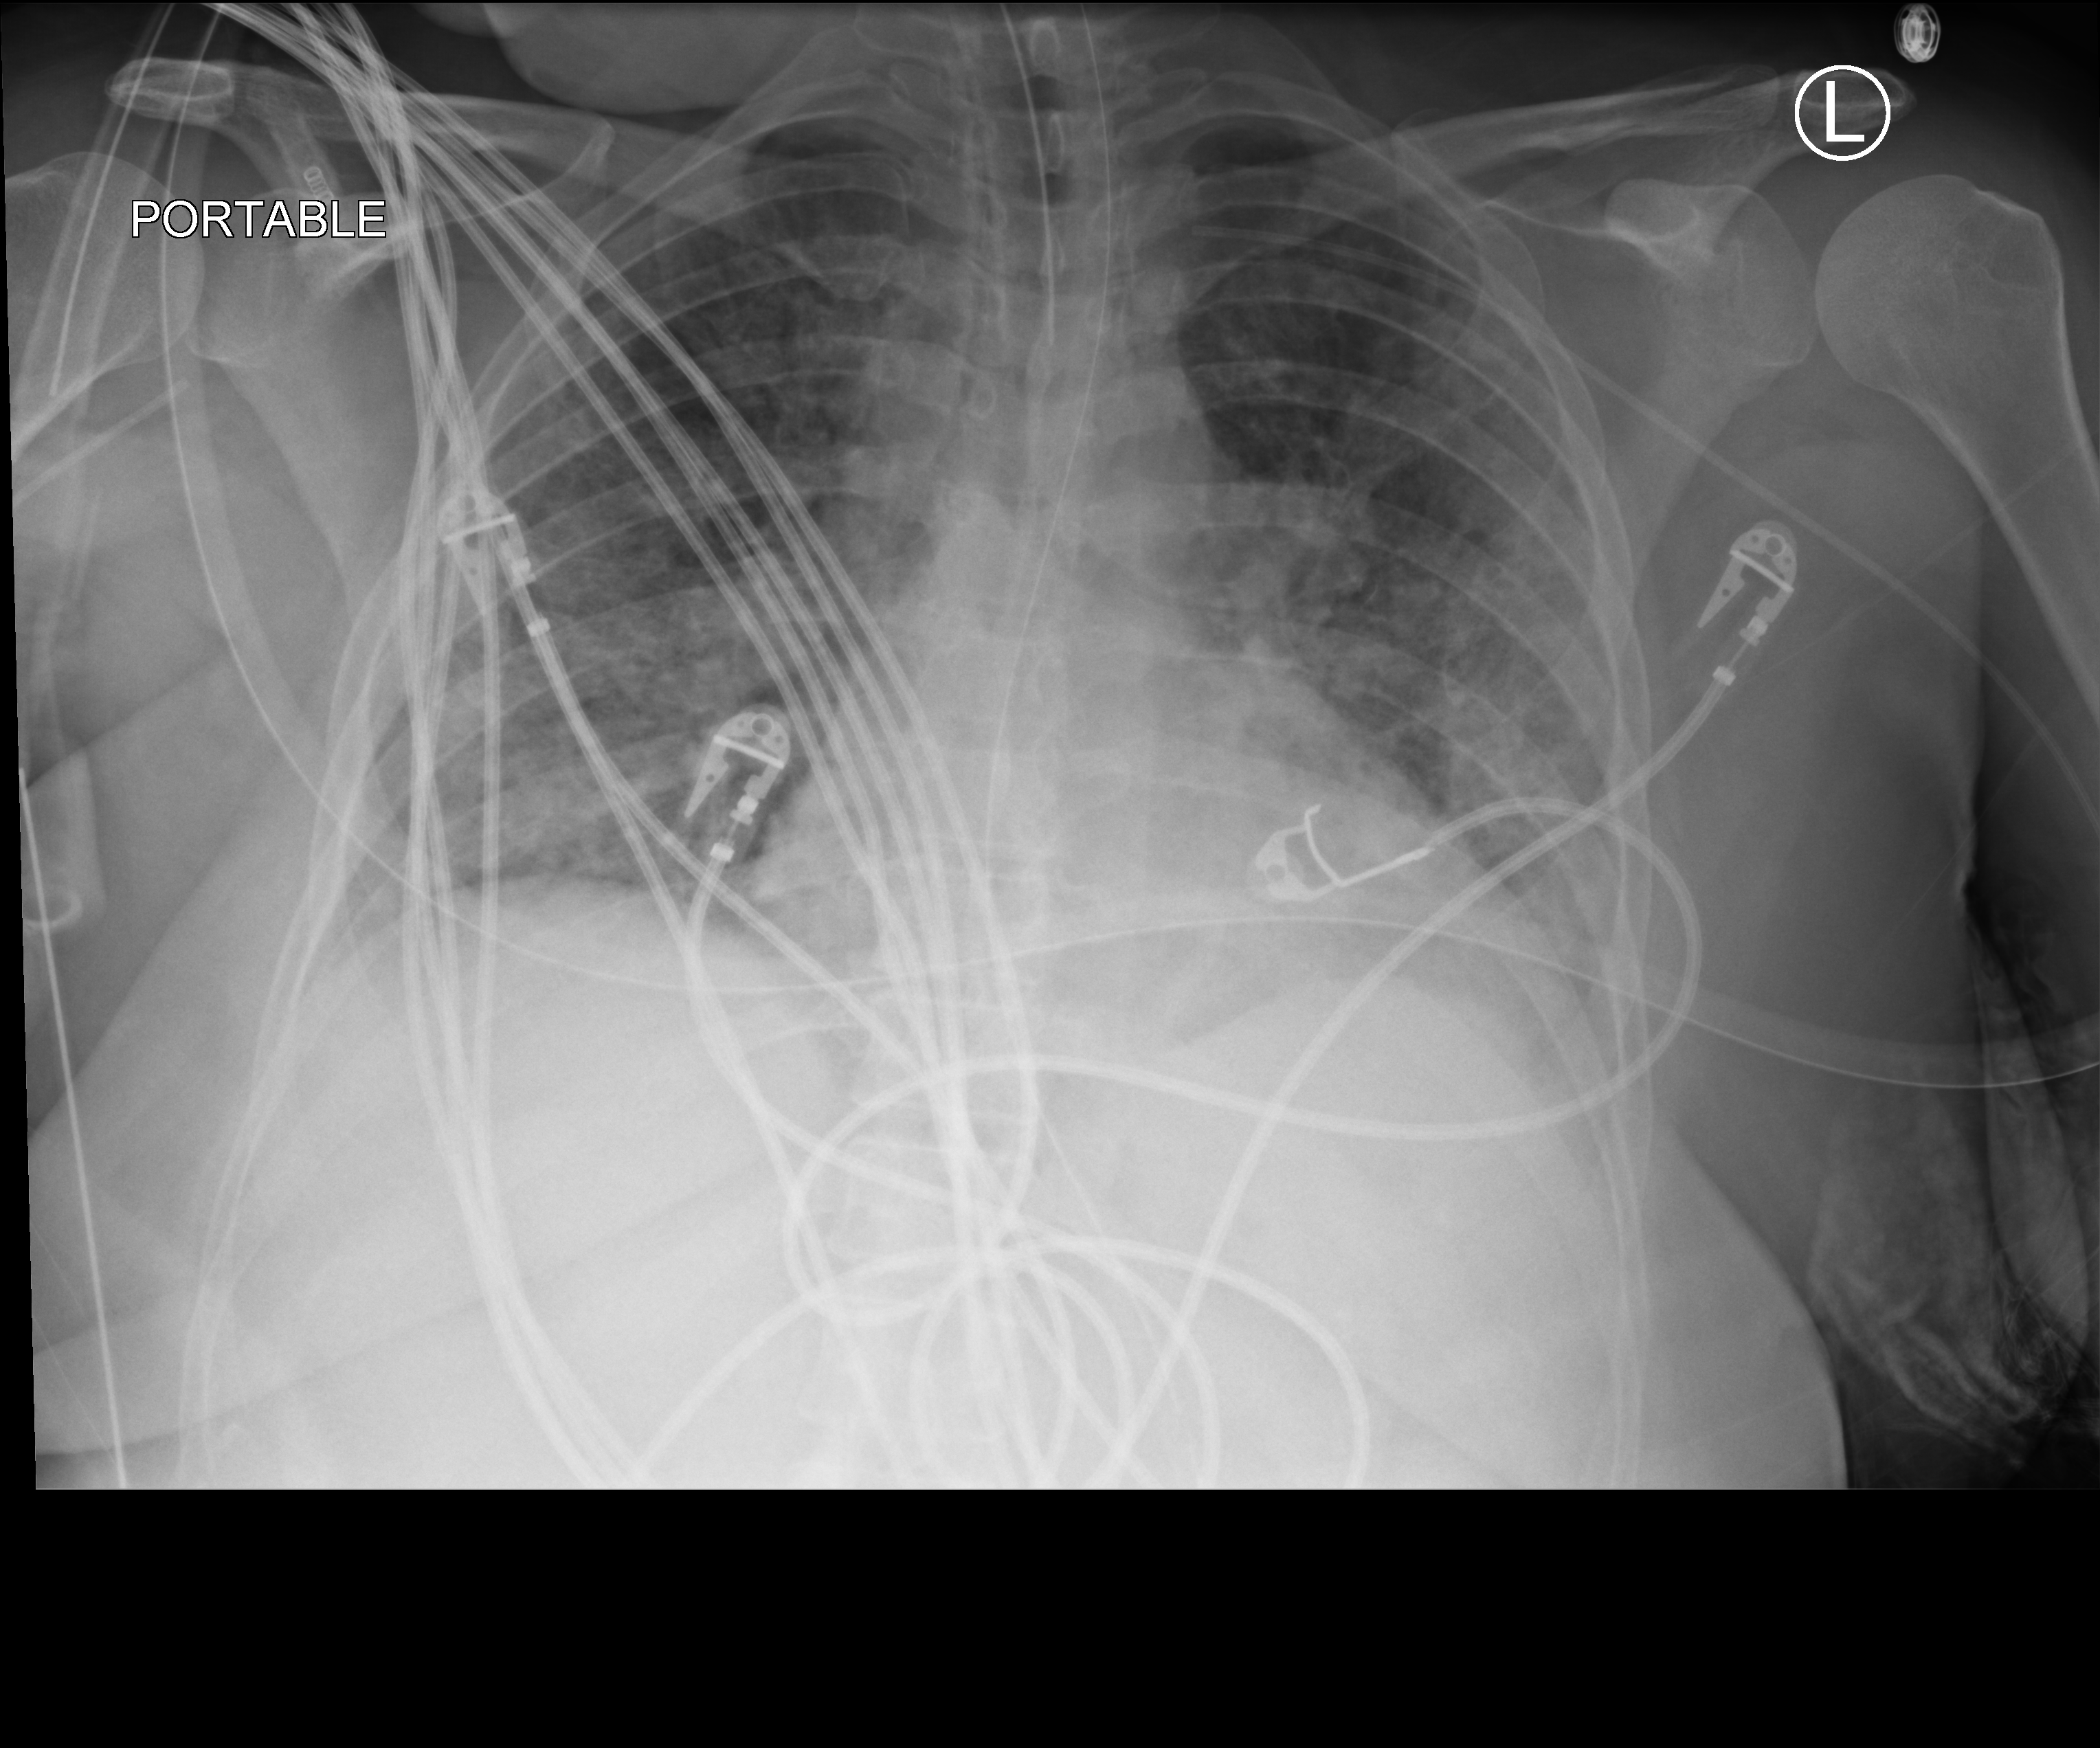
Bedside chest radiograph (computed radiography). Patient hospitalised with COVID-19; female, aged 18–59 years.
Hospital-stay facts (about this admission, not read from this image; timing relative to this image not recorded):
- length of hospital stay: 31 days